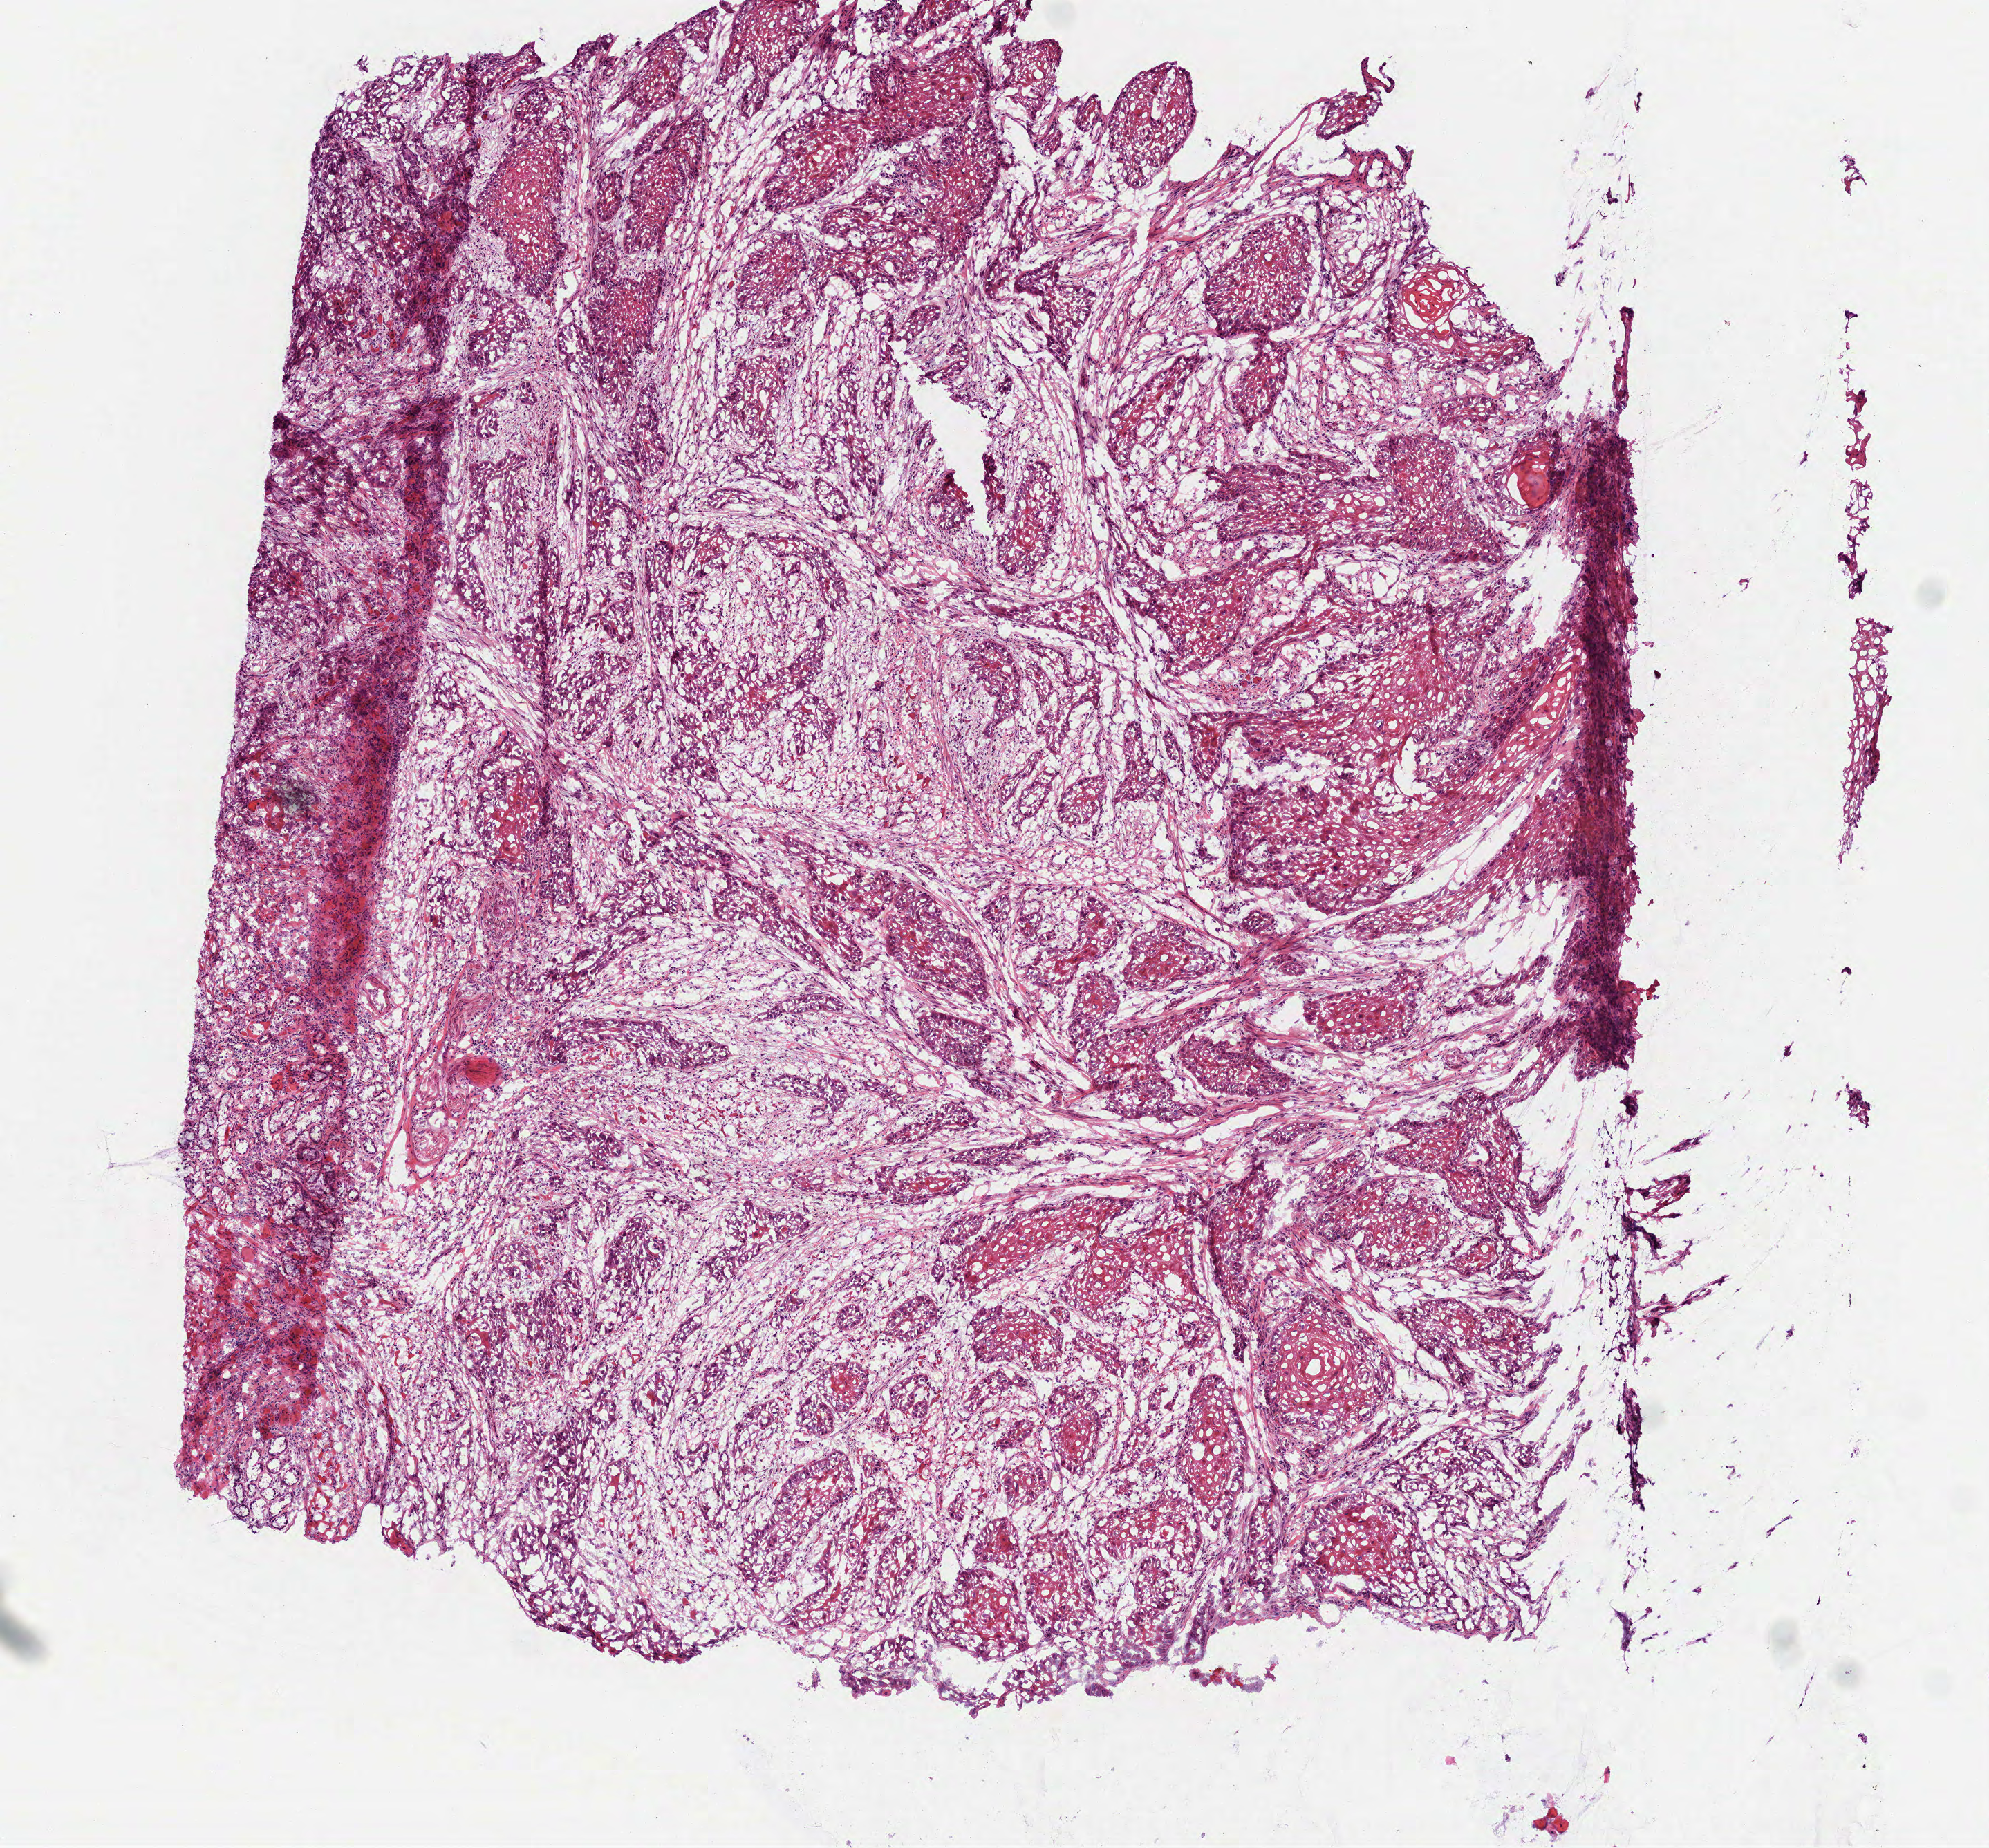
H&E whole-slide image, a low-resolution overview of the entire scanned area, about 5.8 x 5.4 mm (acquisition: 40x scan); frozen section from the bottom of the tissue portion; primary tumour sample from the head and neck. Patient: male, age at initial diagnosis 50 years. Histologic grade: G2 (moderately differentiated). Composition of this section per pathologist review: tumour cells 70%, tumour nuclei 70%, normal cells 0%, stromal cells 30%, necrosis 0%.
Laterality: right. Histologic diagnosis: Squamous cell carcinoma, NOS (tongue, NOS). AJCC pathologic stage: III (7th edition).